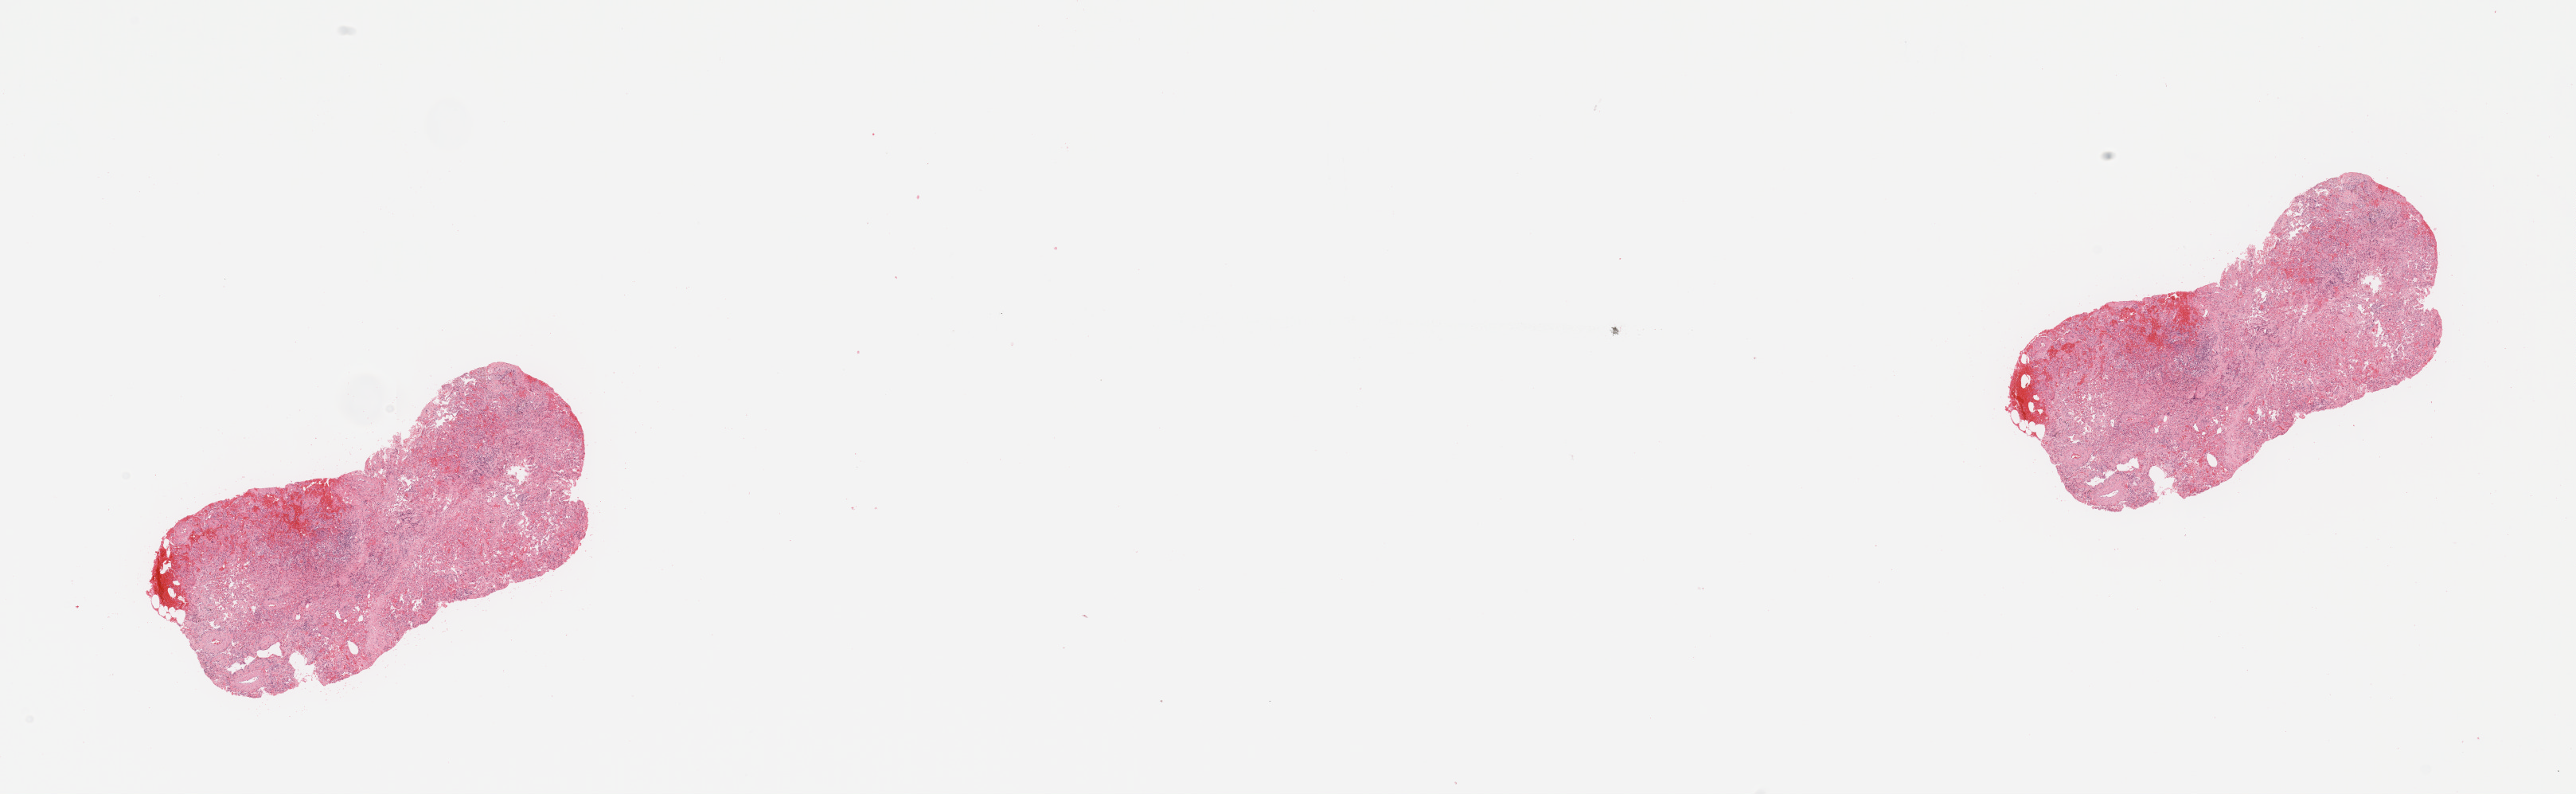
Hematoxylin and eosin (H&E) stained whole-slide image — whole scanned area (about 25.6 x 7.9 mm, slide scanned at 20x) shown as a low-resolution overview; normal (non-tumour) tissue sample, lung. Patient: male, age 71 years.
This section: normal (non-tumour) tissue from the same patient. Patient diagnosis: Adenocarcinoma, NOS.